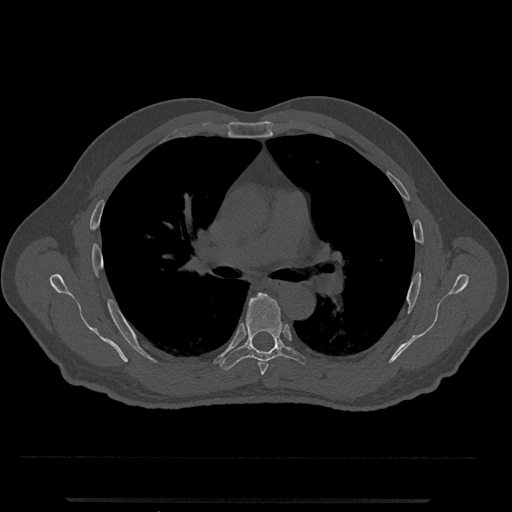
CT including the spine, one axial slice. Slice 749 of 797 in the series (ordered by position). 120 kVp. Bone window (W 1800 / L 400 HU). 512 × 512 image matrix, field of view 419 × 419 mm. Male patient, age 63 years. Case-level facts recorded for this patient, not image findings: primary cancer: prostate.
Outlined on this slice (semi-automatically segmented with operator editing):
- T5 vertebra: bounding box (x1, y1, x2, y2) in pixels: (258, 361, 269, 375)
- T6 vertebra: (220, 293, 306, 371)